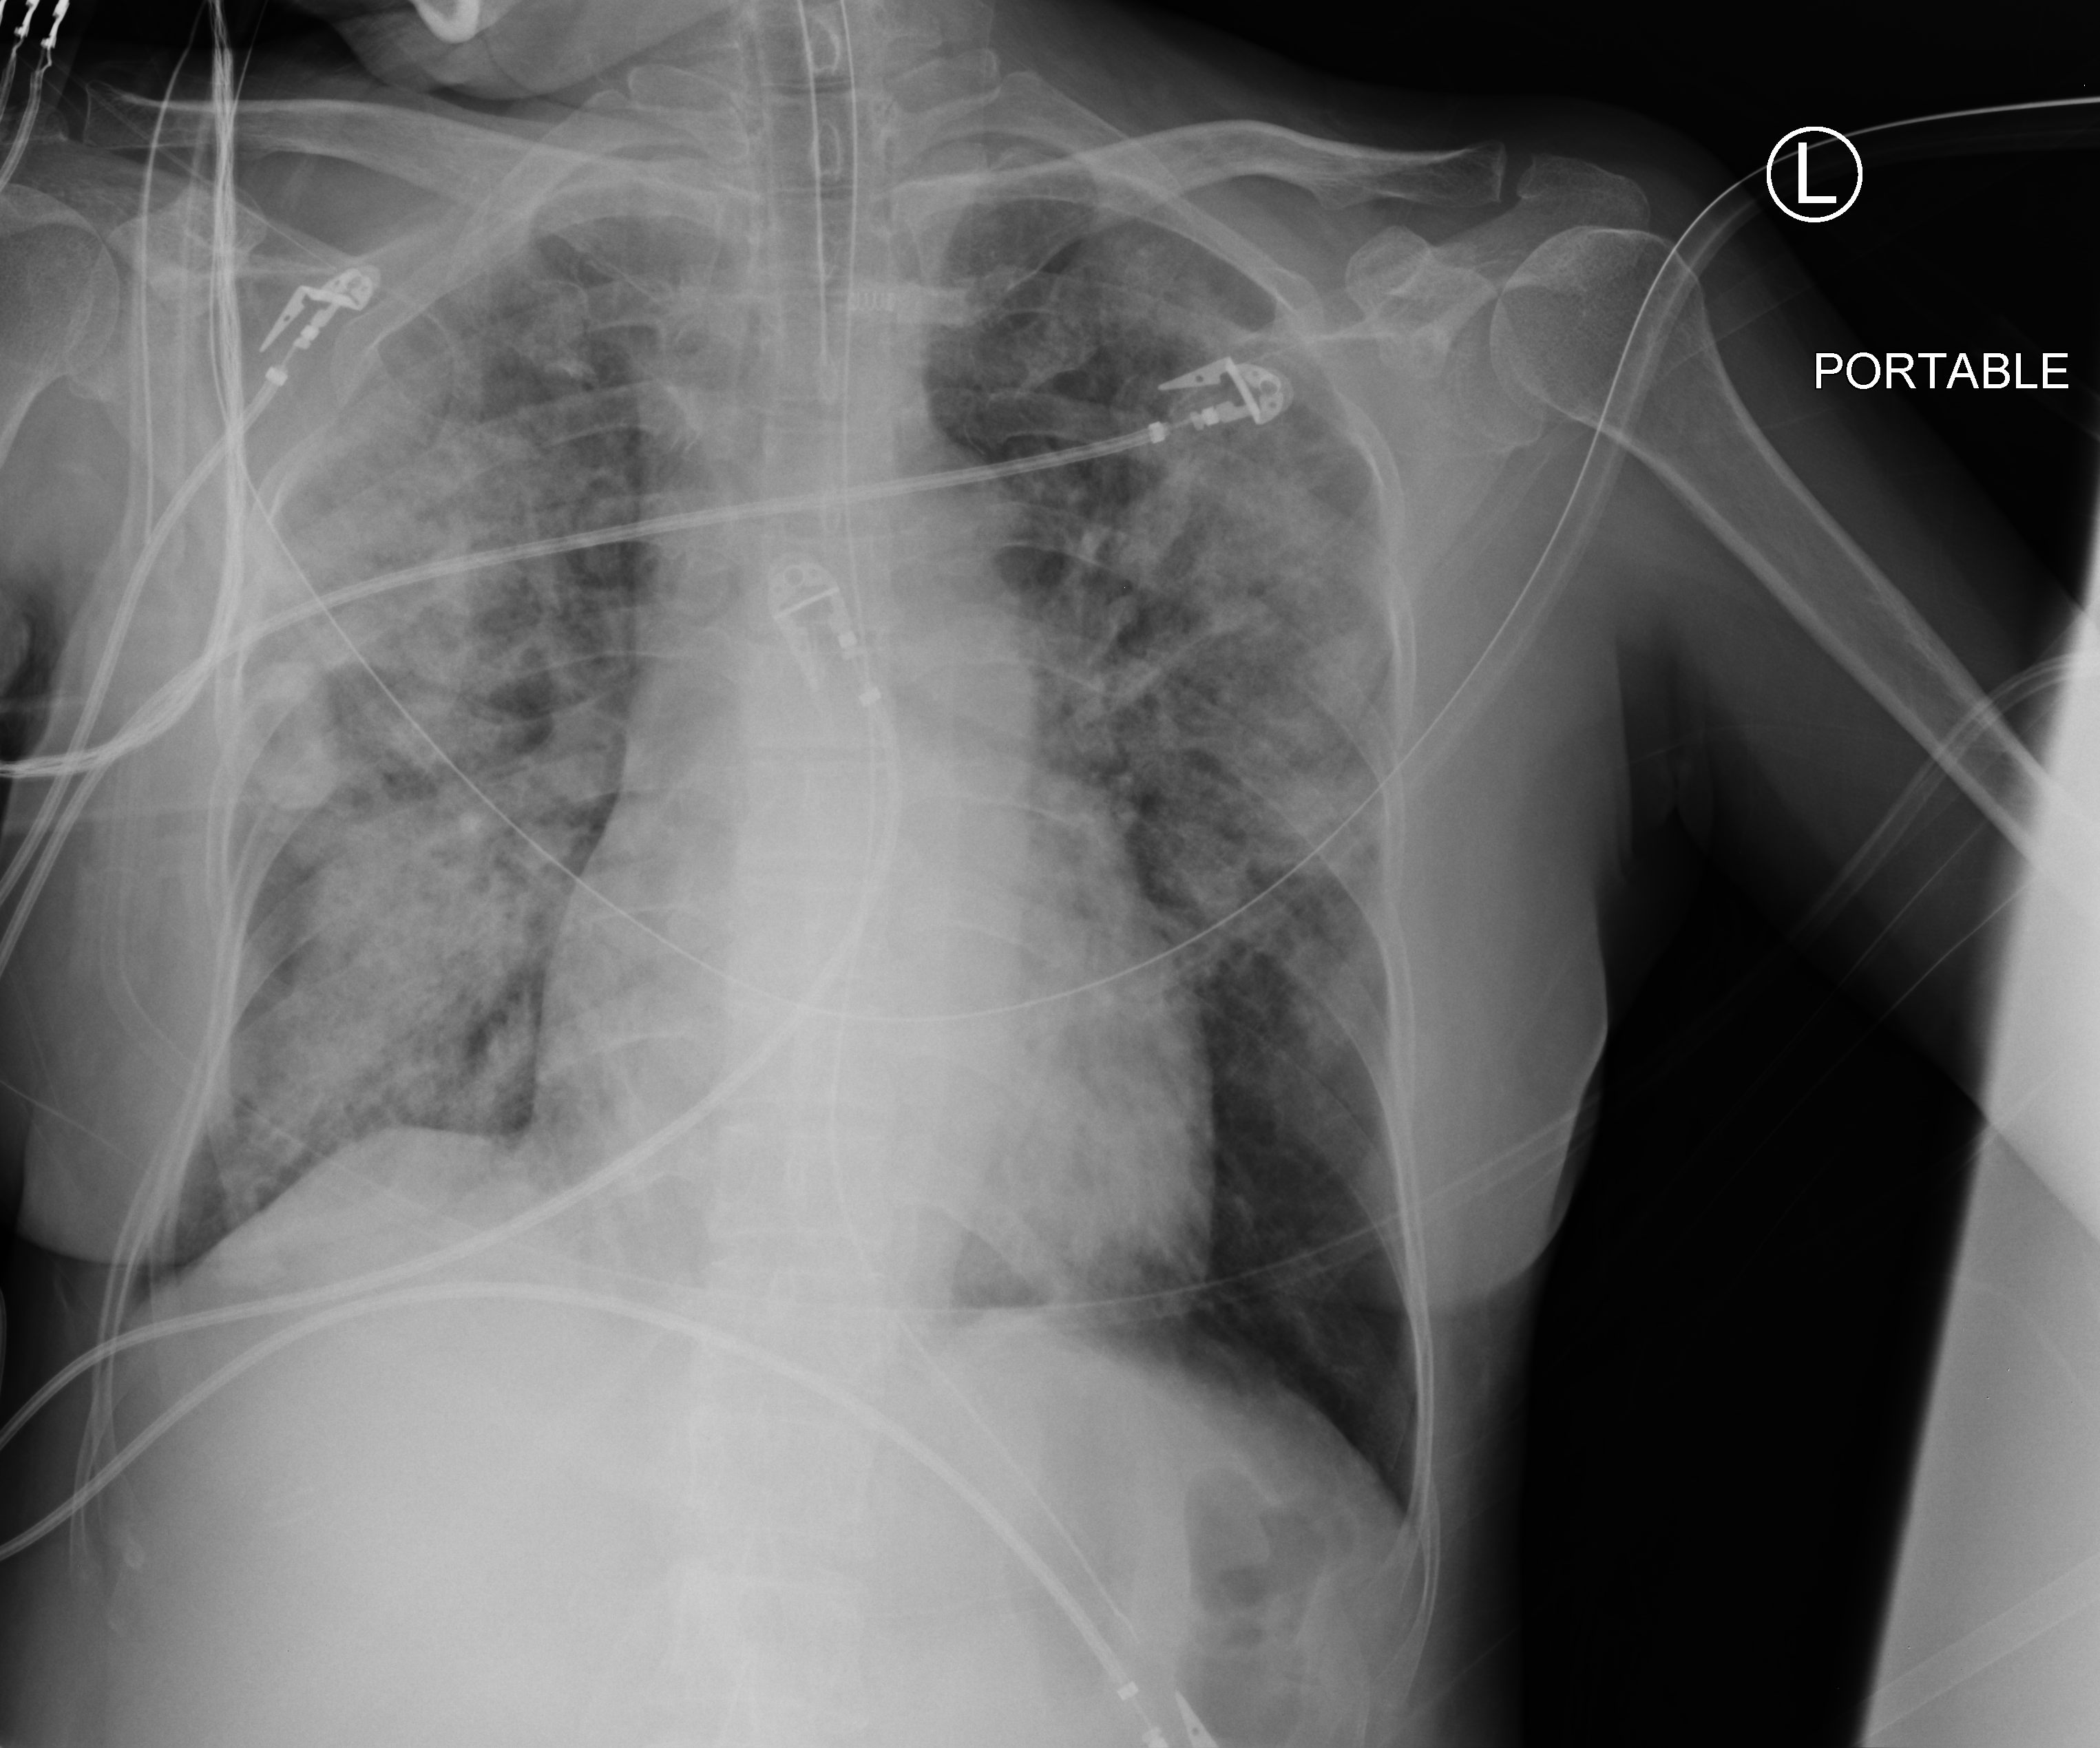
Portable chest radiograph. Patient hospitalised with COVID-19; female, aged 60–74 years.
Admission-level facts for this patient (not findings on this image; timing relative to this image not recorded):
- mechanically ventilated during this hospital stay: yes
- admitted to intensive care during this hospital stay: yes
- chronic kidney disease (admission record): no